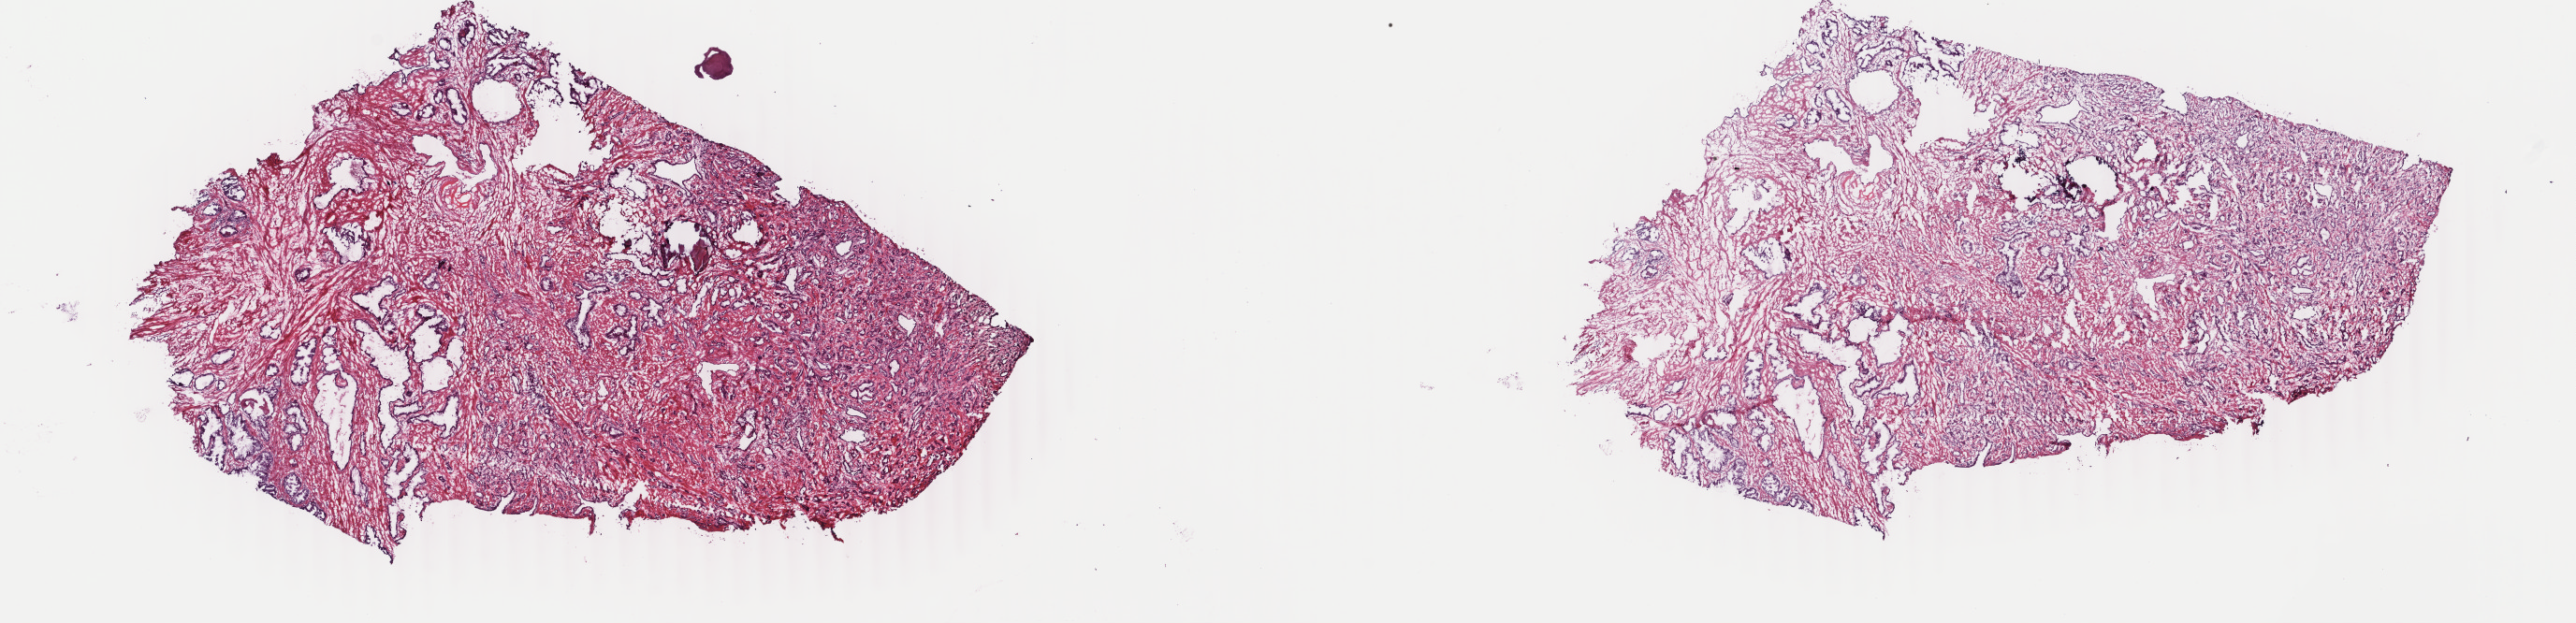
H&E-stained whole-slide image, shown as a low-resolution overview of the whole scanned area (about 21.9 x 5.3 mm, slide scanned at 40x), frozen section from the top of the tissue portion, primary tumour sample from the prostate. Patient: male, age at initial diagnosis 64 years. Gleason score: 7 (3+4). Composition of this section per pathologist review: tumour cells 50%, tumour nuclei 65%, normal cells 15%, stromal cells 35%, necrosis 0%. Infiltration values recorded for this section: lymphocyte infiltration 0%, monocyte infiltration 0%, neutrophil infiltration 0%.
Pathologic diagnosis: Adenocarcinoma, NOS (prostate gland). Lymph nodes positive (case pathology): 0 of 6 examined.